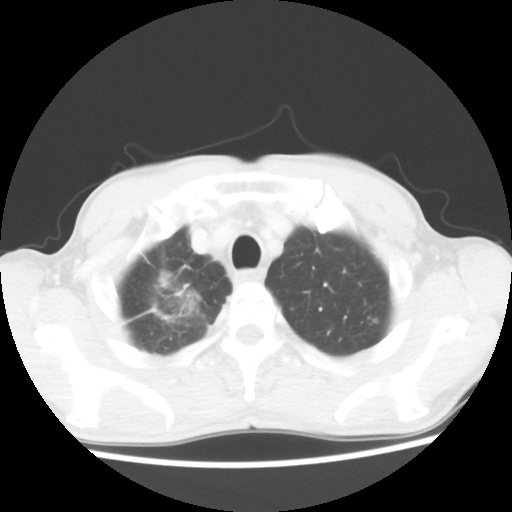
Chest CT, one axial slice; position 46 of 52 along the scan axis; reconstruction kernel STANDARD; lung window (W 1500 / L -600 HU); 5 mm slice thickness; 512 × 512 image matrix, field of view 323 × 323 mm. Male patient, age 66 years. From the clinical record (not read from this slice): clinical TNM (as recorded): T2 N0 M1a.
Outlined on this slice (bounding box drawn by a radiologist):
- lung tumour (recorded histology: adenocarcinoma): box from (x=140, y=267) to (x=208, y=323) px